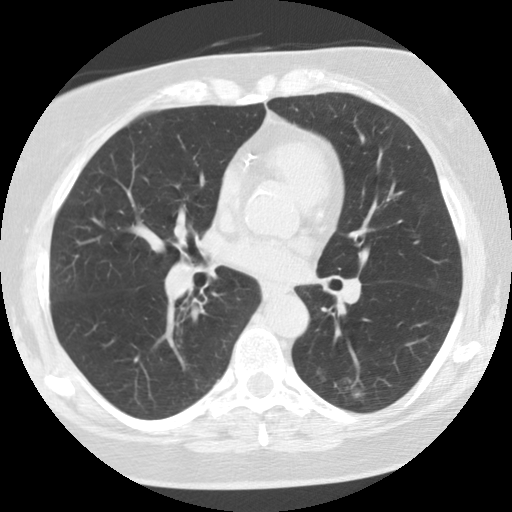
Axial slice from a low-dose chest CT screening exam, baseline screening round, lung window (W 1500 / L -600 HU), standard (soft-tissue) reconstruction kernel (STANDARD), slice 61 of 115 in the series. Female participant, aged 59 years at enrolment.
Expert reader's lesion annotation, bounding box [x1, y1, x2, y2] px = [297, 352, 371, 419]. The screening reader recorded 5 non-calcified nodules or masses ≥4 mm on this exam (right upper lobe, right lower lobe, left lower lobe, right lower lobe, left lower lobe); which of them this box marks is not recorded. Official screen result: positive, change unspecified: nodule(s) >= 4 mm or enlarging nodule(s), mass(es), or other non-specific abnormalities suspicious for lung cancer. Participant outcome: lung cancer diagnosed 707 days after this screen — adenocarcinoma, NOS, left lower lobe, poorly differentiated (G3), stage IA (AJCC 6th edition), 15 mm at pathology.